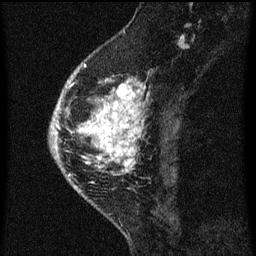
Breast MRI (dynamic contrast-enhanced), one sagittal slice; slice 23 of 60 in the series (ordered by position); dynamic contrast-enhanced series, image 2 of 3 at this slice position (ordered by acquisition); 1.5 T; TE 4.2 ms, TR 8 ms; 256 × 256 image matrix, field of view 180 × 180 mm. Patient: female, 46 years.
Annotated regions visible in this slice (semi-automatic segmentation, software-assisted and operator-edited):
- analysis volume of interest (the breast-tissue region the enhancement analysis was run in; not a lesion): bounding box (x1, y1, x2, y2) in pixels: (60, 68, 145, 195)
- tumour enhancement mask (voxels above the 70 % enhancement threshold inside the analysis volume of interest): (60, 76, 145, 185)